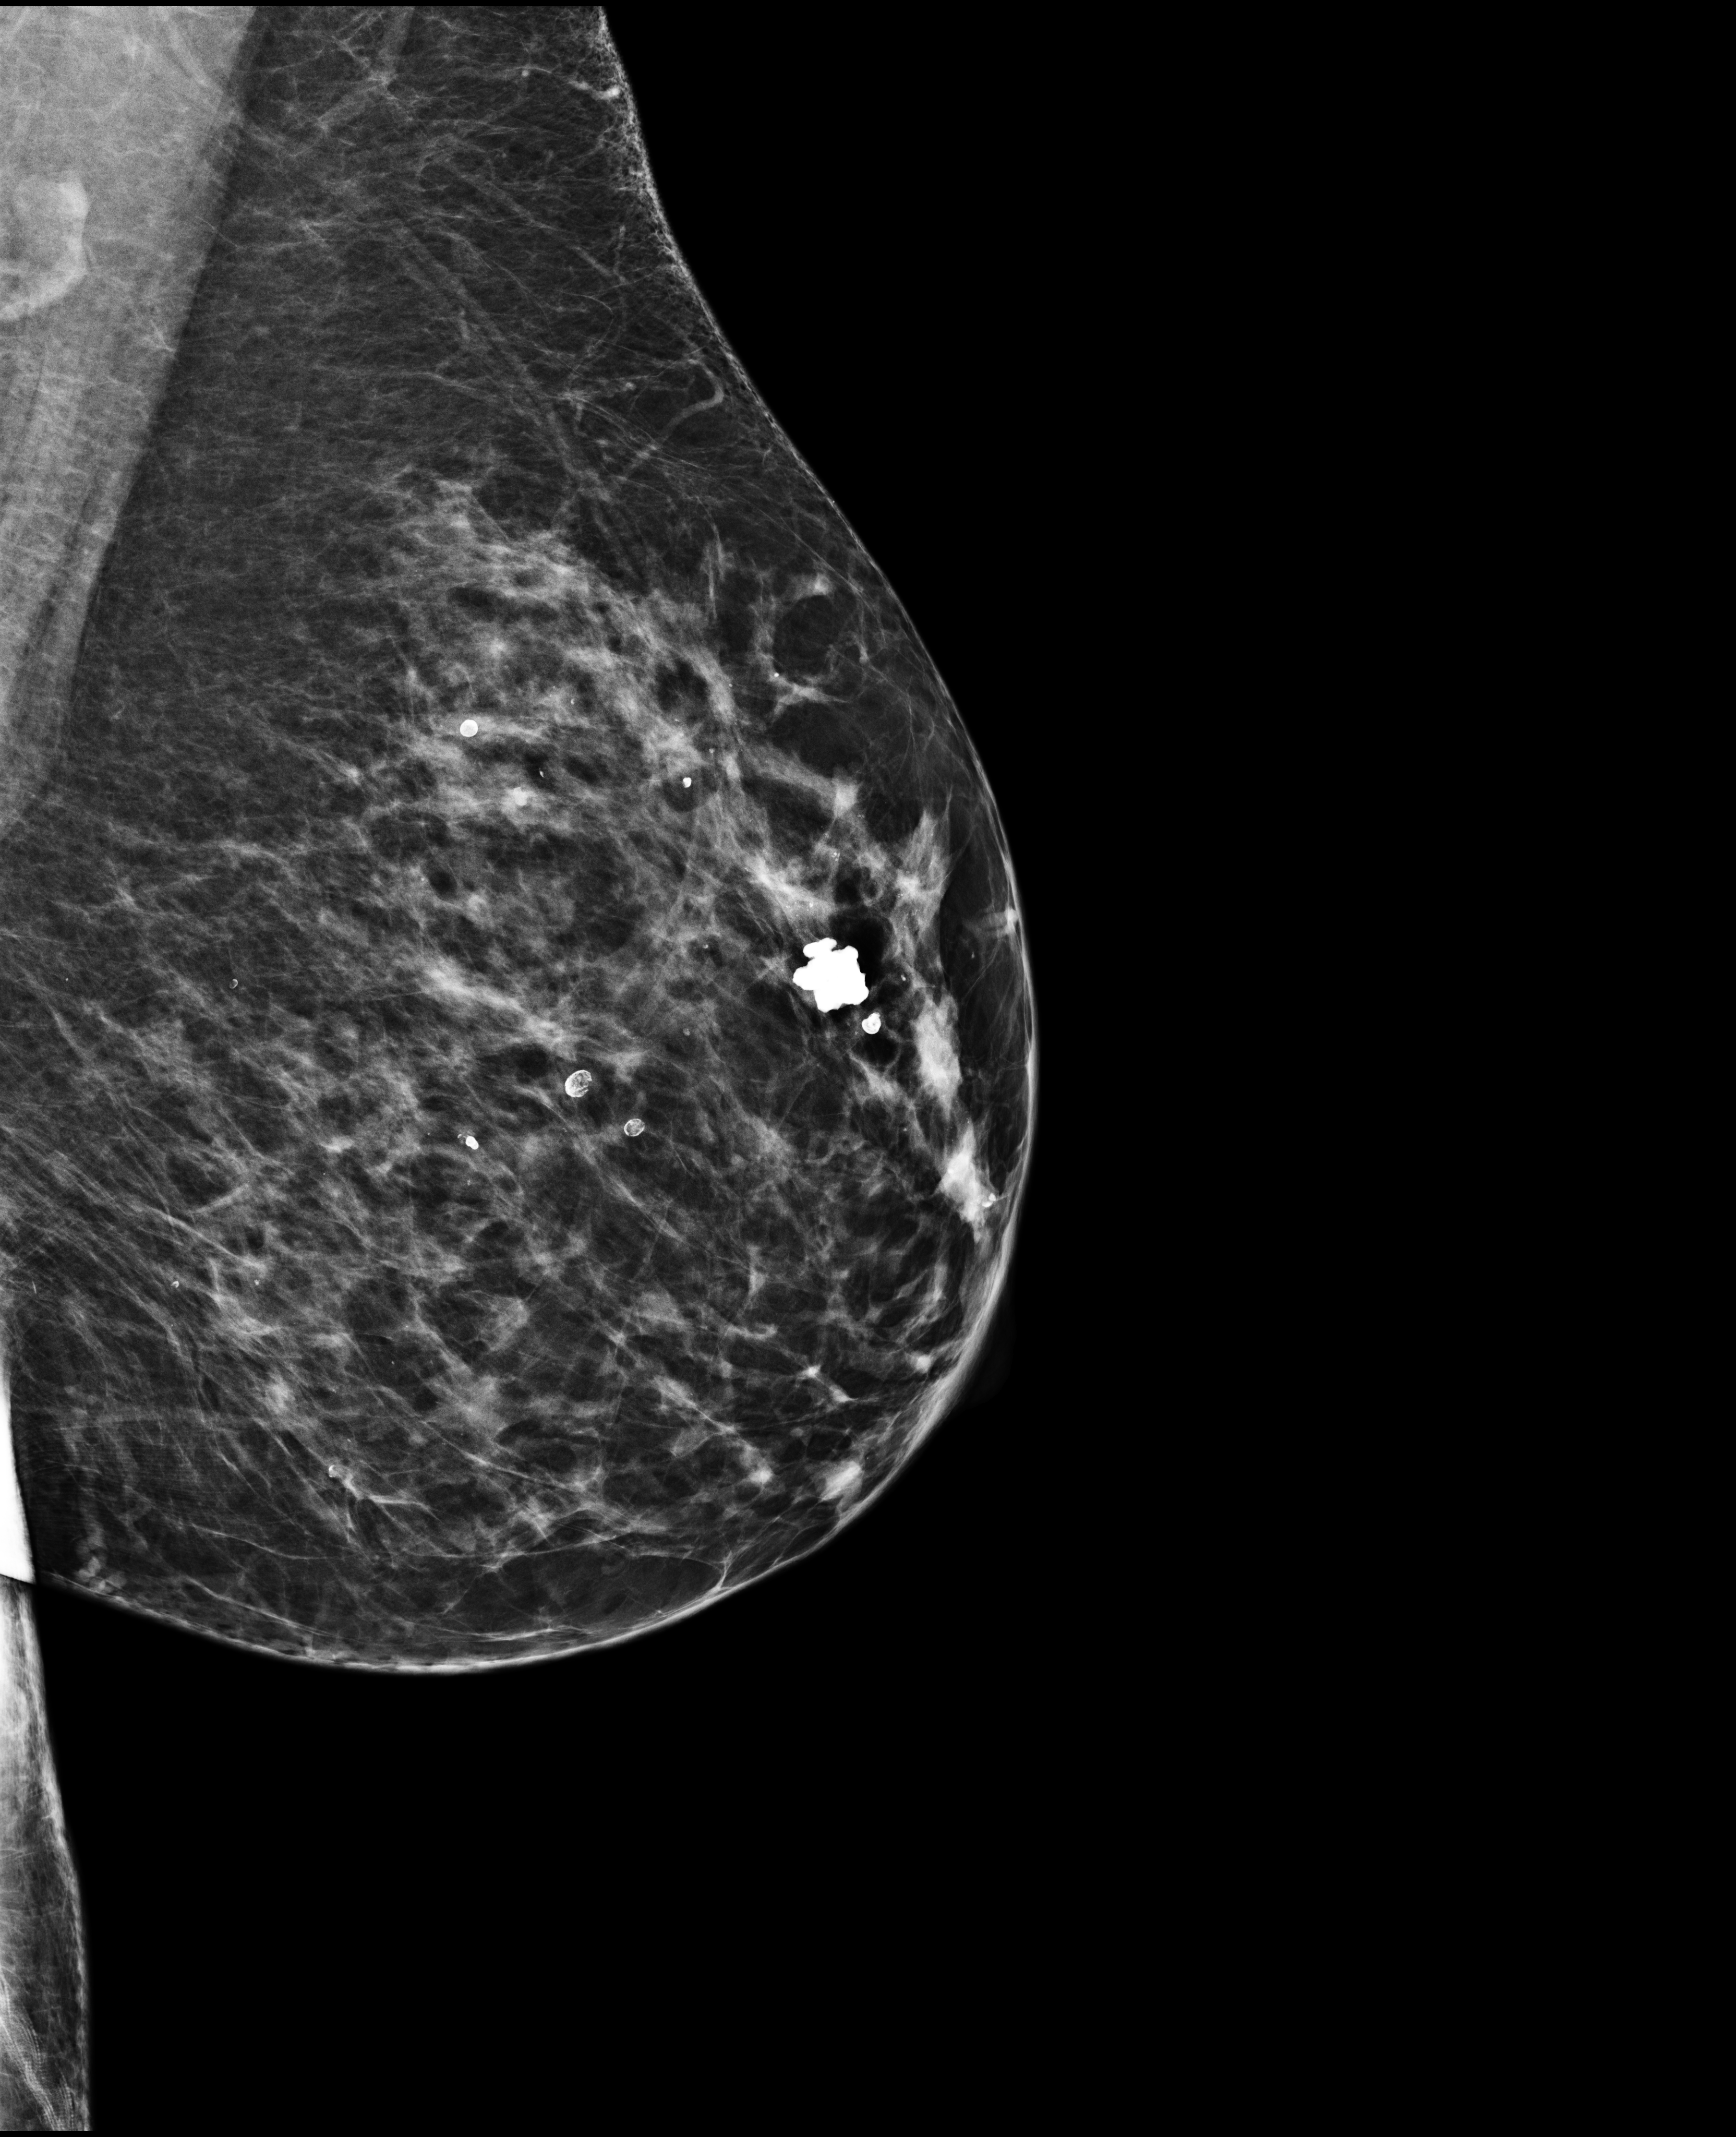
Full-field digital mammogram (FFDM), left breast, mediolateral oblique (MLO) view, annual screening mammography examination. Patient: female, 65 years.
- breast density at the screening exam (both breasts): heterogeneously dense (BI-RADS density category c)
- final BI-RADS assessment for this screening round (tomosynthesis exam, both breasts): category 2
- recall: no recall after this screen